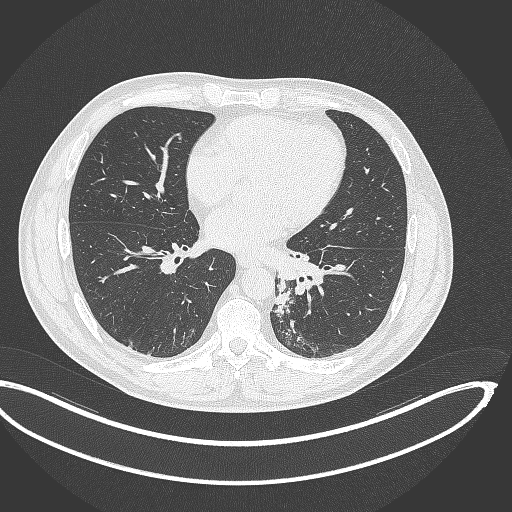
Chest CT, one axial slice; slice 149 of 362 in the series (ordered by position); lung window (W 1500 / L -600 HU); 512 × 512 image matrix, field of view 442 × 442 mm. Male patient, age 50 years. From the clinical record (not read from this slice): clinical TNM (as recorded): T2a N3 M0.
Structures marked on this image (bounding box drawn by a radiologist):
- lung tumour (recorded histology: squamous cell carcinoma): bounding box (x1, y1, x2, y2) in pixels: (270, 279, 295, 316)